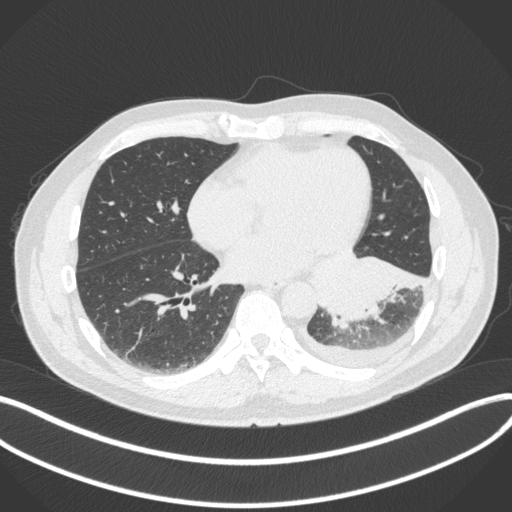
Chest CT, one axial slice; position 140 of 350 along the scan axis; reconstruction kernel B31f; 120 kVp; lung window (W 1500 / L -600 HU); 1 mm slice thickness; 512 × 512 image matrix, field of view 400 × 400 mm. Patient: male, 58 years. From the clinical record (not read from this slice): clinical TNM (as recorded): T3 N1 M1b; histopathological grade: G3.
Outlined on this slice (rectangle marked by the reading radiologist):
- lung tumour (recorded histology: small cell carcinoma): bounding box [x1, y1, x2, y2] px = [321, 252, 428, 328]